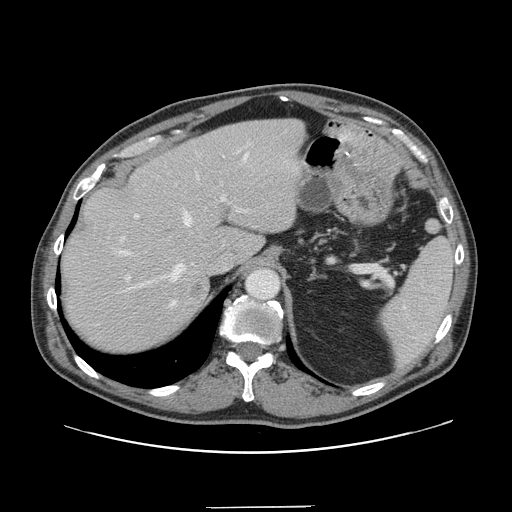
Contrast-enhanced abdominal CT, one axial slice. Slice 109 of 139 in the series (ordered by position). 120 kVp. Soft-tissue window (W 400 / L 40 HU). 512 × 512 image matrix, field of view 397 × 397 mm. Male patient, age 64 years. Case-level facts recorded for this patient, not image findings: diagnosis: colorectal cancer liver metastases, imaged before liver resection.
Outlined on this slice (manually delineated by an expert):
- hepatic veins: box from (x=119, y=153) to (x=248, y=306) px
- liver: (x=62, y=120)–(x=304, y=350)
- planned liver remnant (the part of the liver to remain after resection): (x=62, y=121)–(x=271, y=350)
- portal vein (with intrahepatic branches): (x=120, y=143)–(x=249, y=289)